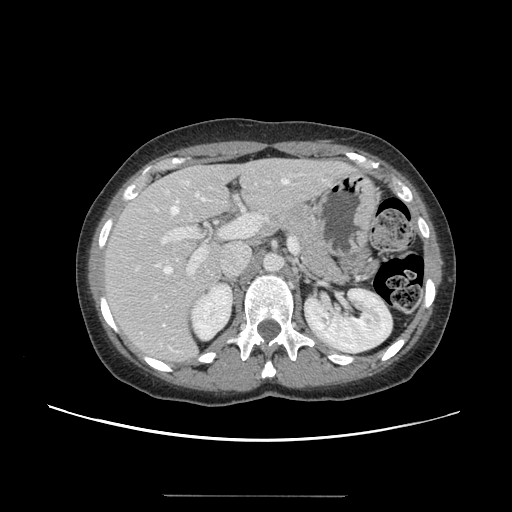
Contrast-enhanced abdominal CT, one axial slice. Position 83 of 144 along the scan axis. Soft-tissue window (W 400 / L 40 HU). 2.5 mm slice thickness. 512 × 512 image matrix, field of view 380 × 380 mm. Female patient, age 53 years. Case-level facts recorded for this patient, not image findings: diagnosis: colorectal cancer liver metastases, imaged before liver resection.
Annotated regions visible in this slice (expert manual segmentation):
- hepatic veins: bounding box (x1, y1, x2, y2) in pixels: (163, 179, 288, 326)
- liver: (106, 160, 347, 362)
- planned liver remnant (the part of the liver to remain after resection): (107, 159, 315, 298)
- portal vein (with intrahepatic branches): (136, 182, 299, 299)